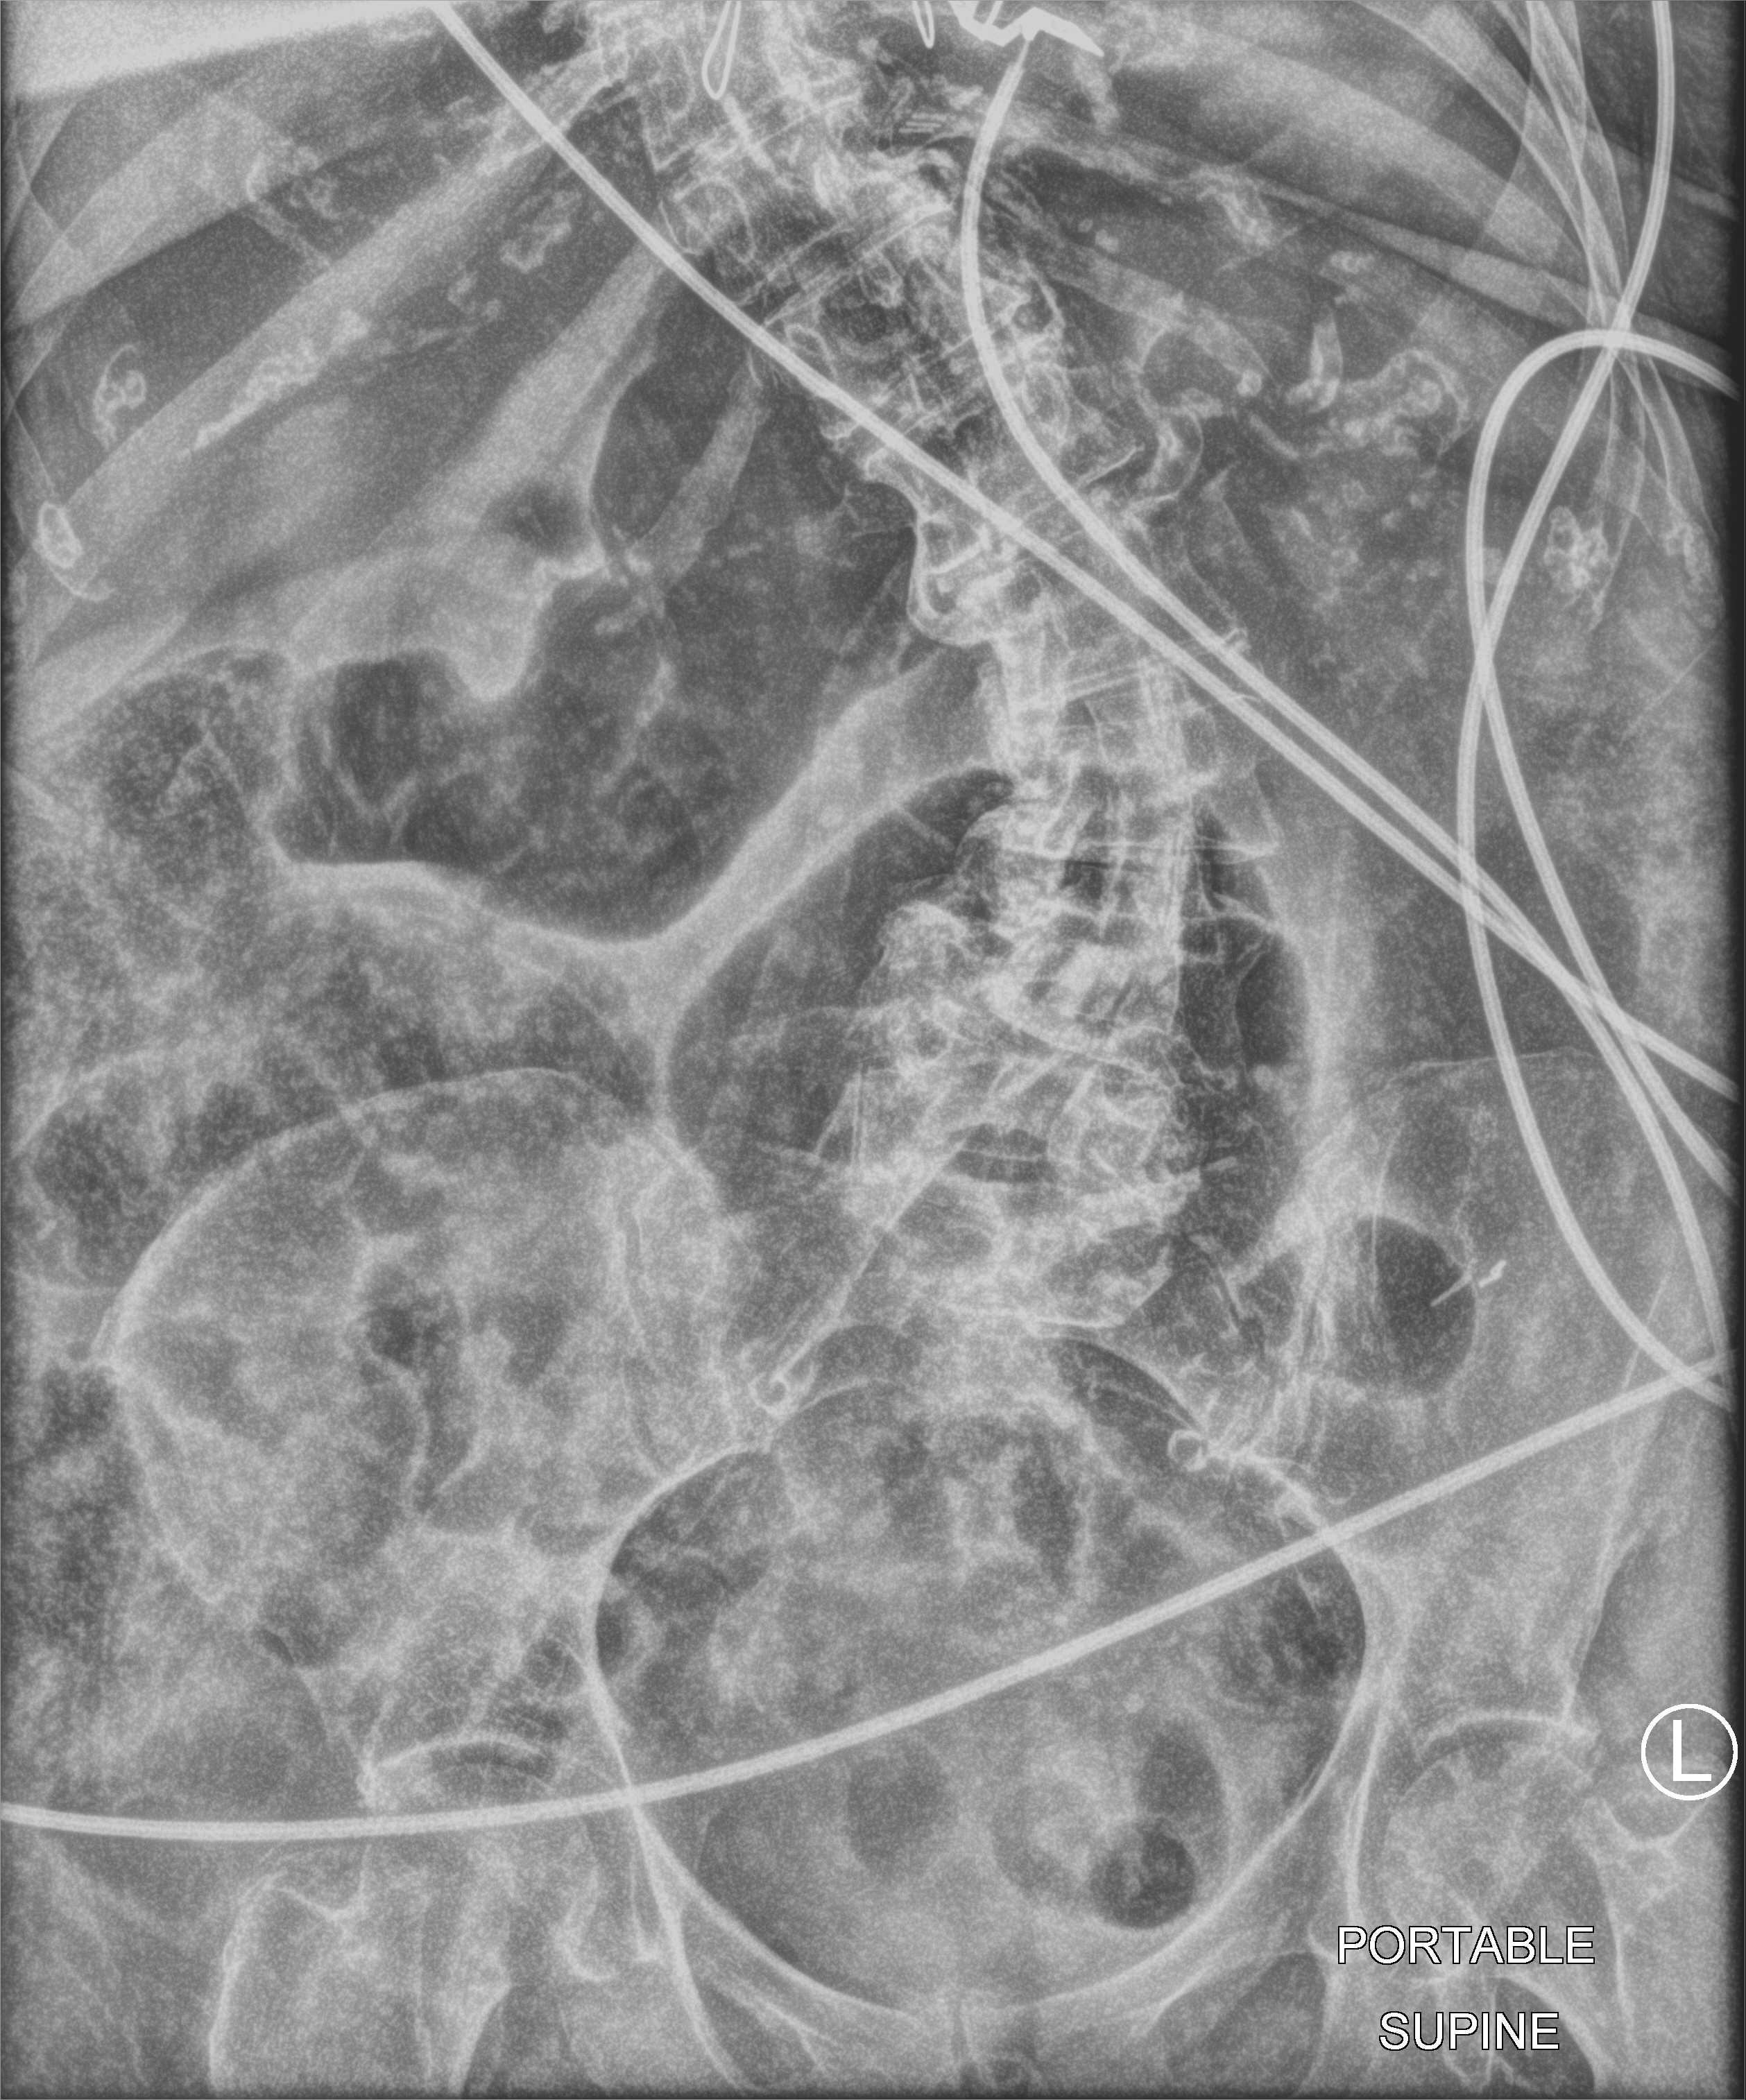
Bedside abdomen radiograph (computed radiography); anteroposterior (AP) projection. Patient hospitalised with COVID-19; female, aged 75–90 years.
Hospital-stay facts (about this admission, not read from this image; timing relative to this image not recorded):
- mechanically ventilated during this hospital stay: no
- admitted to intensive care during this hospital stay: no